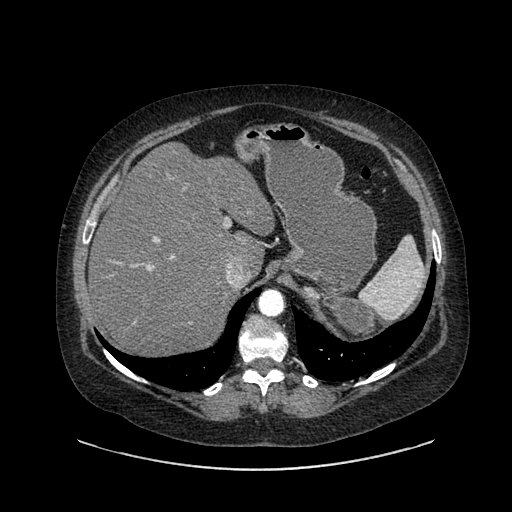
Contrast-enhanced abdominal CT, one axial slice. Position 637 of 769 along the scan axis. Intravenous contrast given. Soft-tissue window (W 400 / L 40 HU). 0.62 mm slice thickness. 512 × 512 image matrix, field of view 460 × 460 mm. Female patient, age 61 years. Case-level facts recorded for this patient, not image findings: diagnosis: adrenocortical carcinoma; tumour side: left adrenal; tumour size at pathology: 13 cm; Ki-67 index: 79 %; stage (as recorded): 2.
Annotated regions visible in this slice (semi-automatically segmented with operator editing):
- mass: bounding box <312,285,376,339> (left, top, right, bottom; pixels)